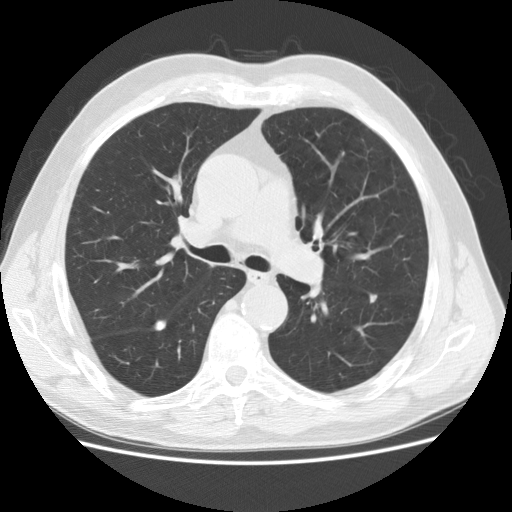
Low-dose screening chest CT, axial slice; first (baseline) screen; lung window (W 1500 / L -600 HU); slice 64 of 155 in the series. Male participant, aged 73 years at enrolment. Current smoker at enrolment.
- Expert-annotated lung lesion, box from (x=350, y=283) to (x=394, y=314) px.
- No non-calcified nodule or mass ≥4 mm was recorded by the screening reader at this exam.
- Official screen result: negative screen, significant abnormalities not suspicious for lung cancer.
- Participant outcome: lung cancer diagnosed 536 days after this screen (after the second annual screen) — adenocarcinoma, NOS, left lower lobe, poorly differentiated (G3), stage IIA (AJCC 6th edition), 12 mm at pathology.